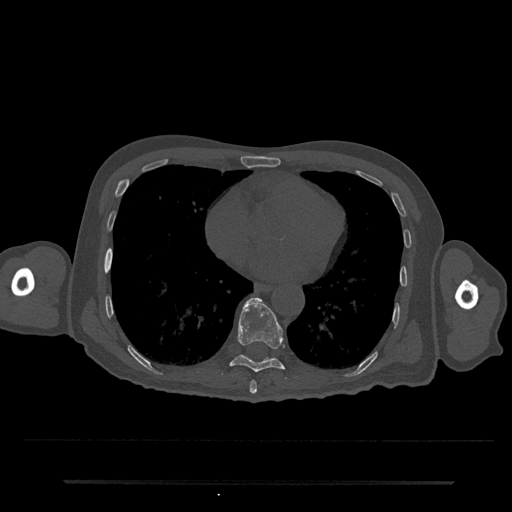
CT including the spine, one axial slice. Slice 364 of 797 in the series (ordered by position). 120 kVp. Bone window (W 1800 / L 400 HU). 0.5 mm slice thickness. 512 × 512 image matrix, field of view 427 × 427 mm. Male patient, age 74 years. From the clinical record (not read from this slice): primary cancer: prostate.
Outlined on this slice (semi-automatic segmentation, software-assisted and operator-edited):
- T8 vertebra: bounding box (x1, y1, x2, y2) in pixels: (249, 380, 257, 394)
- T9 vertebra: (229, 297, 285, 372)